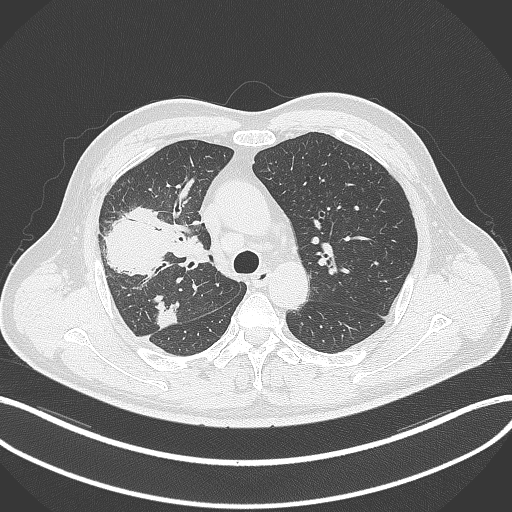
Chest CT, one axial slice. Slice 228 of 348 in the series (ordered by position). Reconstruction kernel B70f. Lung window (W 1500 / L -600 HU). 512 × 512 image matrix, field of view 400 × 400 mm. Patient: male, 55 years. Case-level facts recorded for this patient, not image findings: clinical TNM (as recorded): T3 N2 M1.
Annotated regions visible in this slice (bounding box drawn by a radiologist):
- lung tumour (recorded histology: adenocarcinoma): bounding box [x1, y1, x2, y2] px = [103, 201, 173, 278]